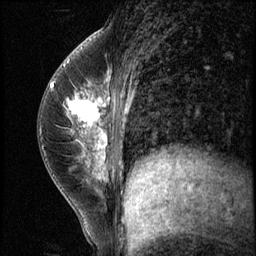
Breast MRI (dynamic contrast-enhanced), one sagittal slice; position 26 of 56 along the scan axis; 3 images stored at this slice position (order not interpretable as contrast timing); 1.5 T; TE 4.2 ms, TR 8.7 ms; 2.5 mm slice thickness; 256 × 256 image matrix, field of view 180 × 180 mm. Patient: female, 35 years. From the clinical record (not read from this slice): setting: breast cancer imaged before/during neoadjuvant chemotherapy; receptor status: HER2-positive.
Outlined on this slice (semi-automatically segmented with operator editing):
- analysis volume of interest (the breast-tissue region the enhancement analysis was run in; not a lesion): bounding box <58,84,138,186> (left, top, right, bottom; pixels)
- tumour enhancement mask (voxels above the 140 % enhancement threshold inside the analysis volume of interest): <66,85,109,178>